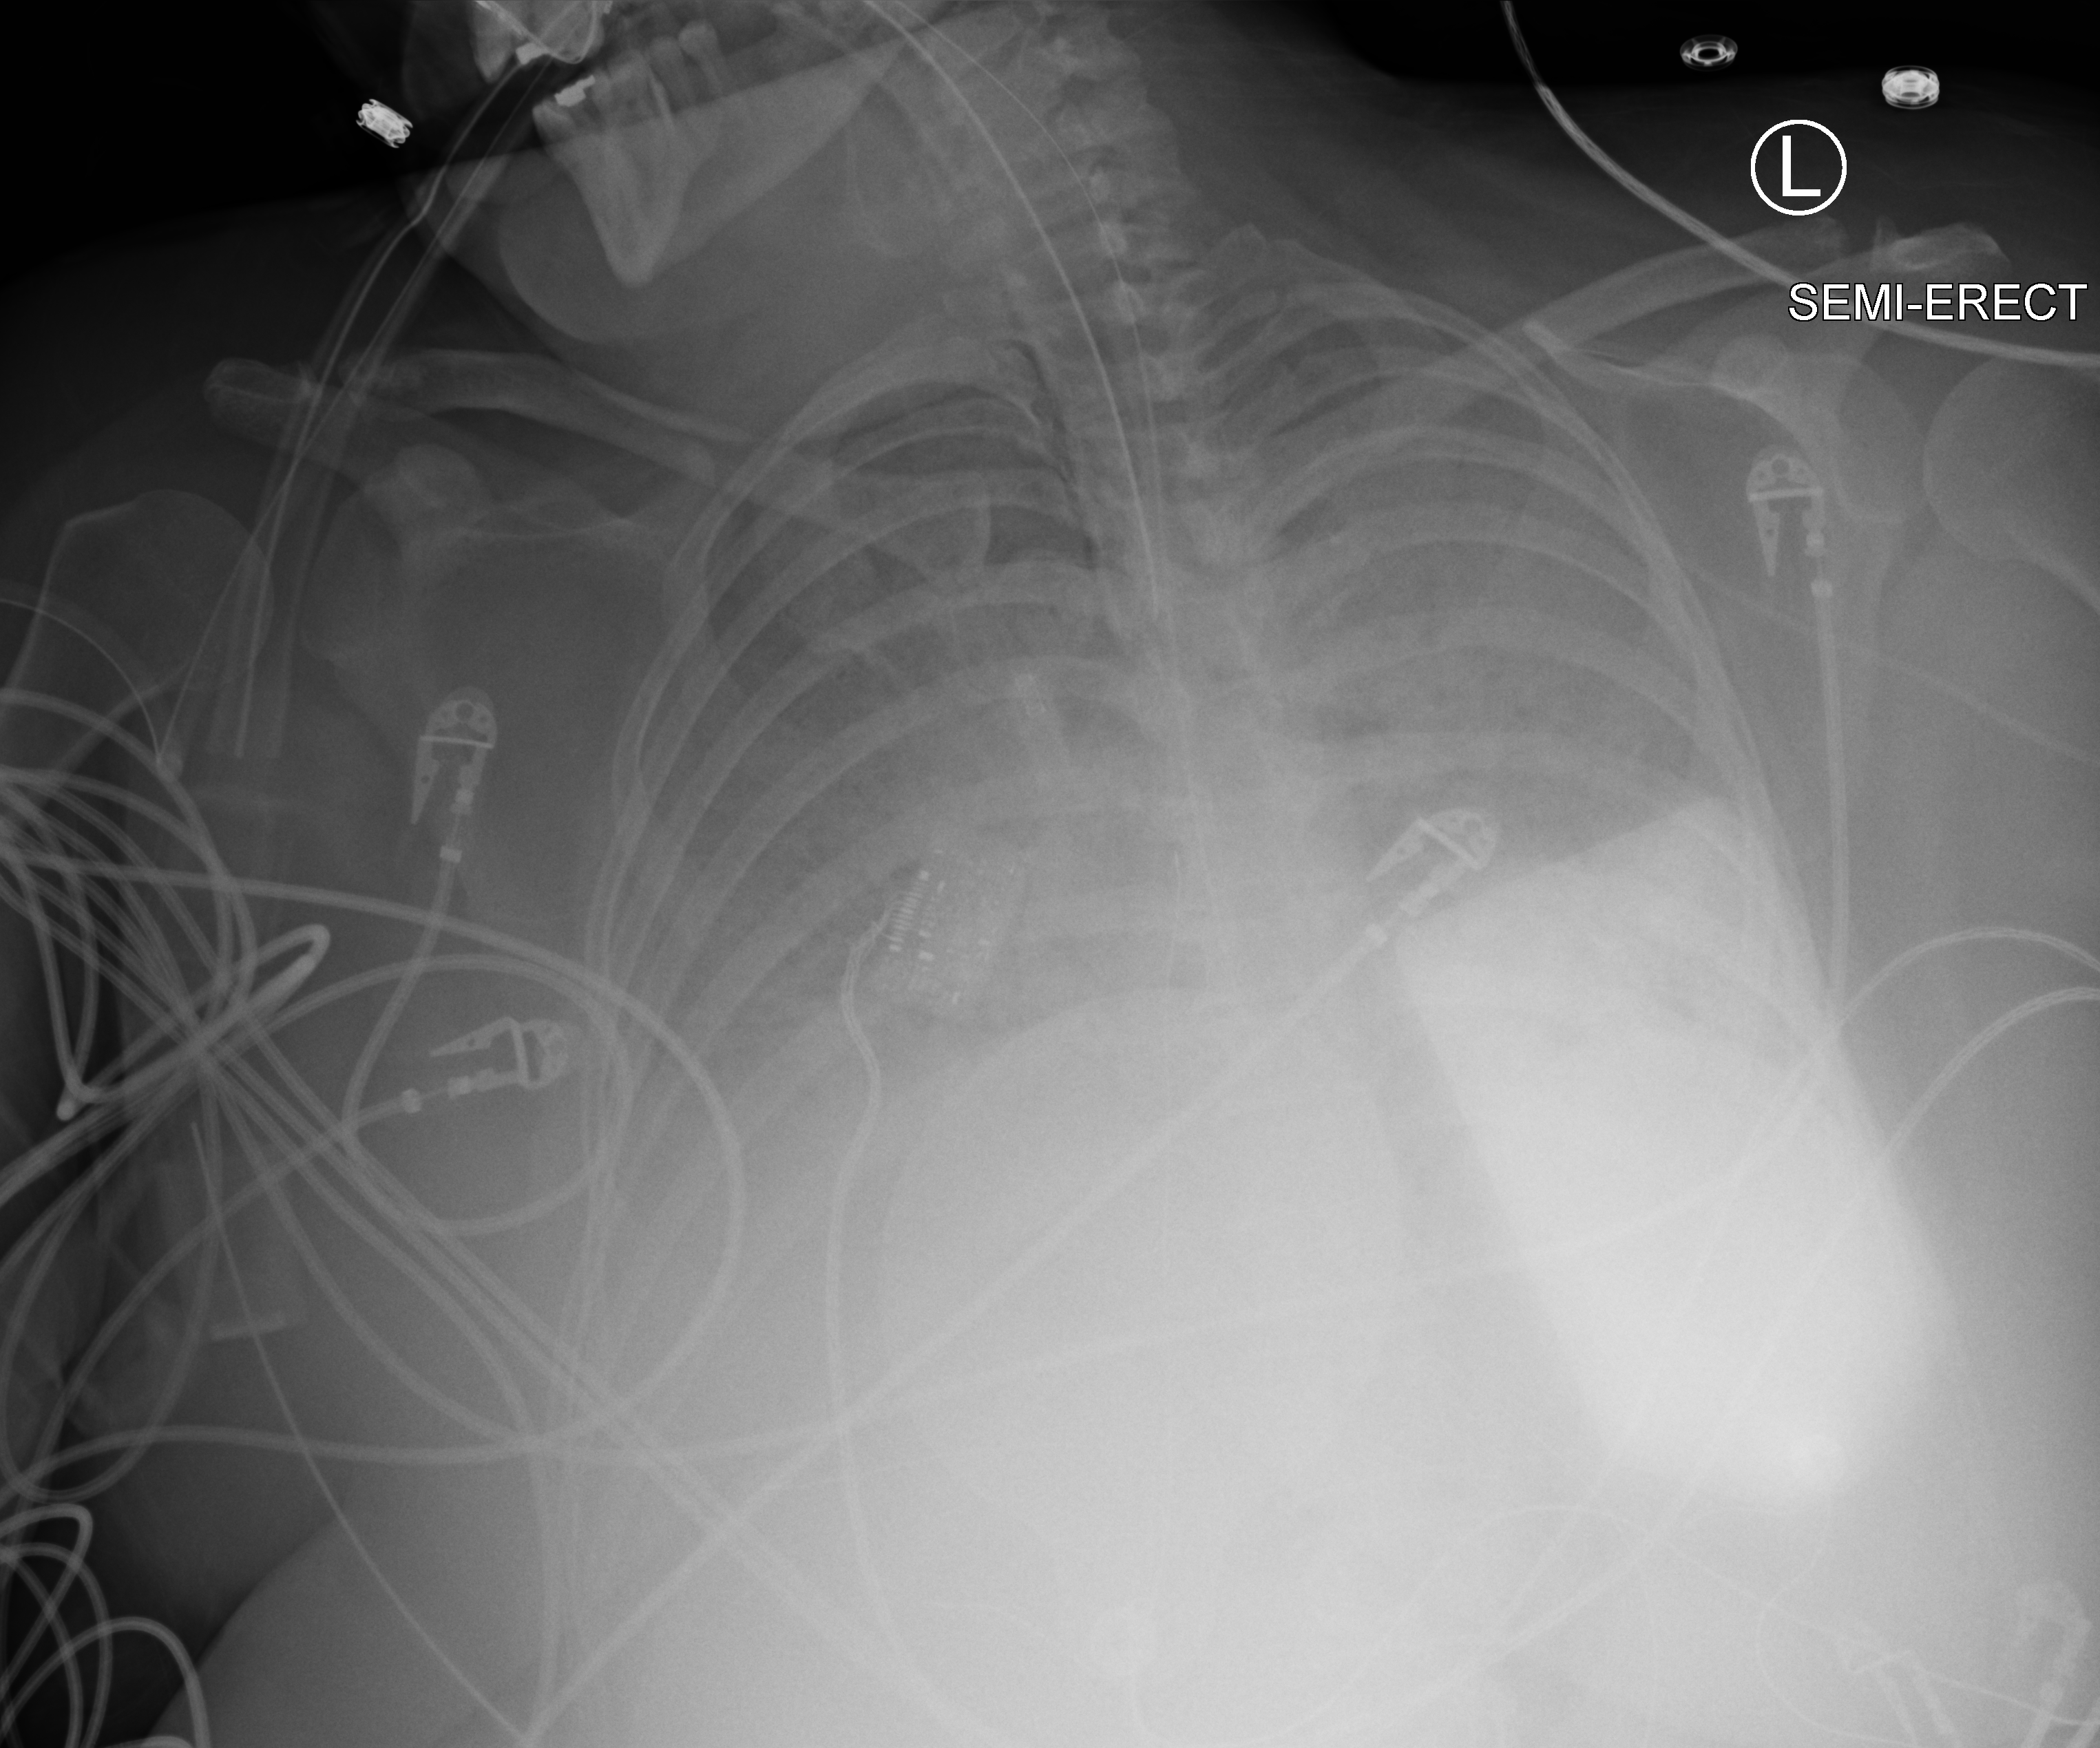
Bedside chest radiograph (computed radiography), anteroposterior (AP) projection. Patient hospitalised with COVID-19; female, aged 18–59 years.
Admission-level facts for this patient (not findings on this image; timing relative to this image not recorded): mechanically ventilated during this hospital stay: yes.